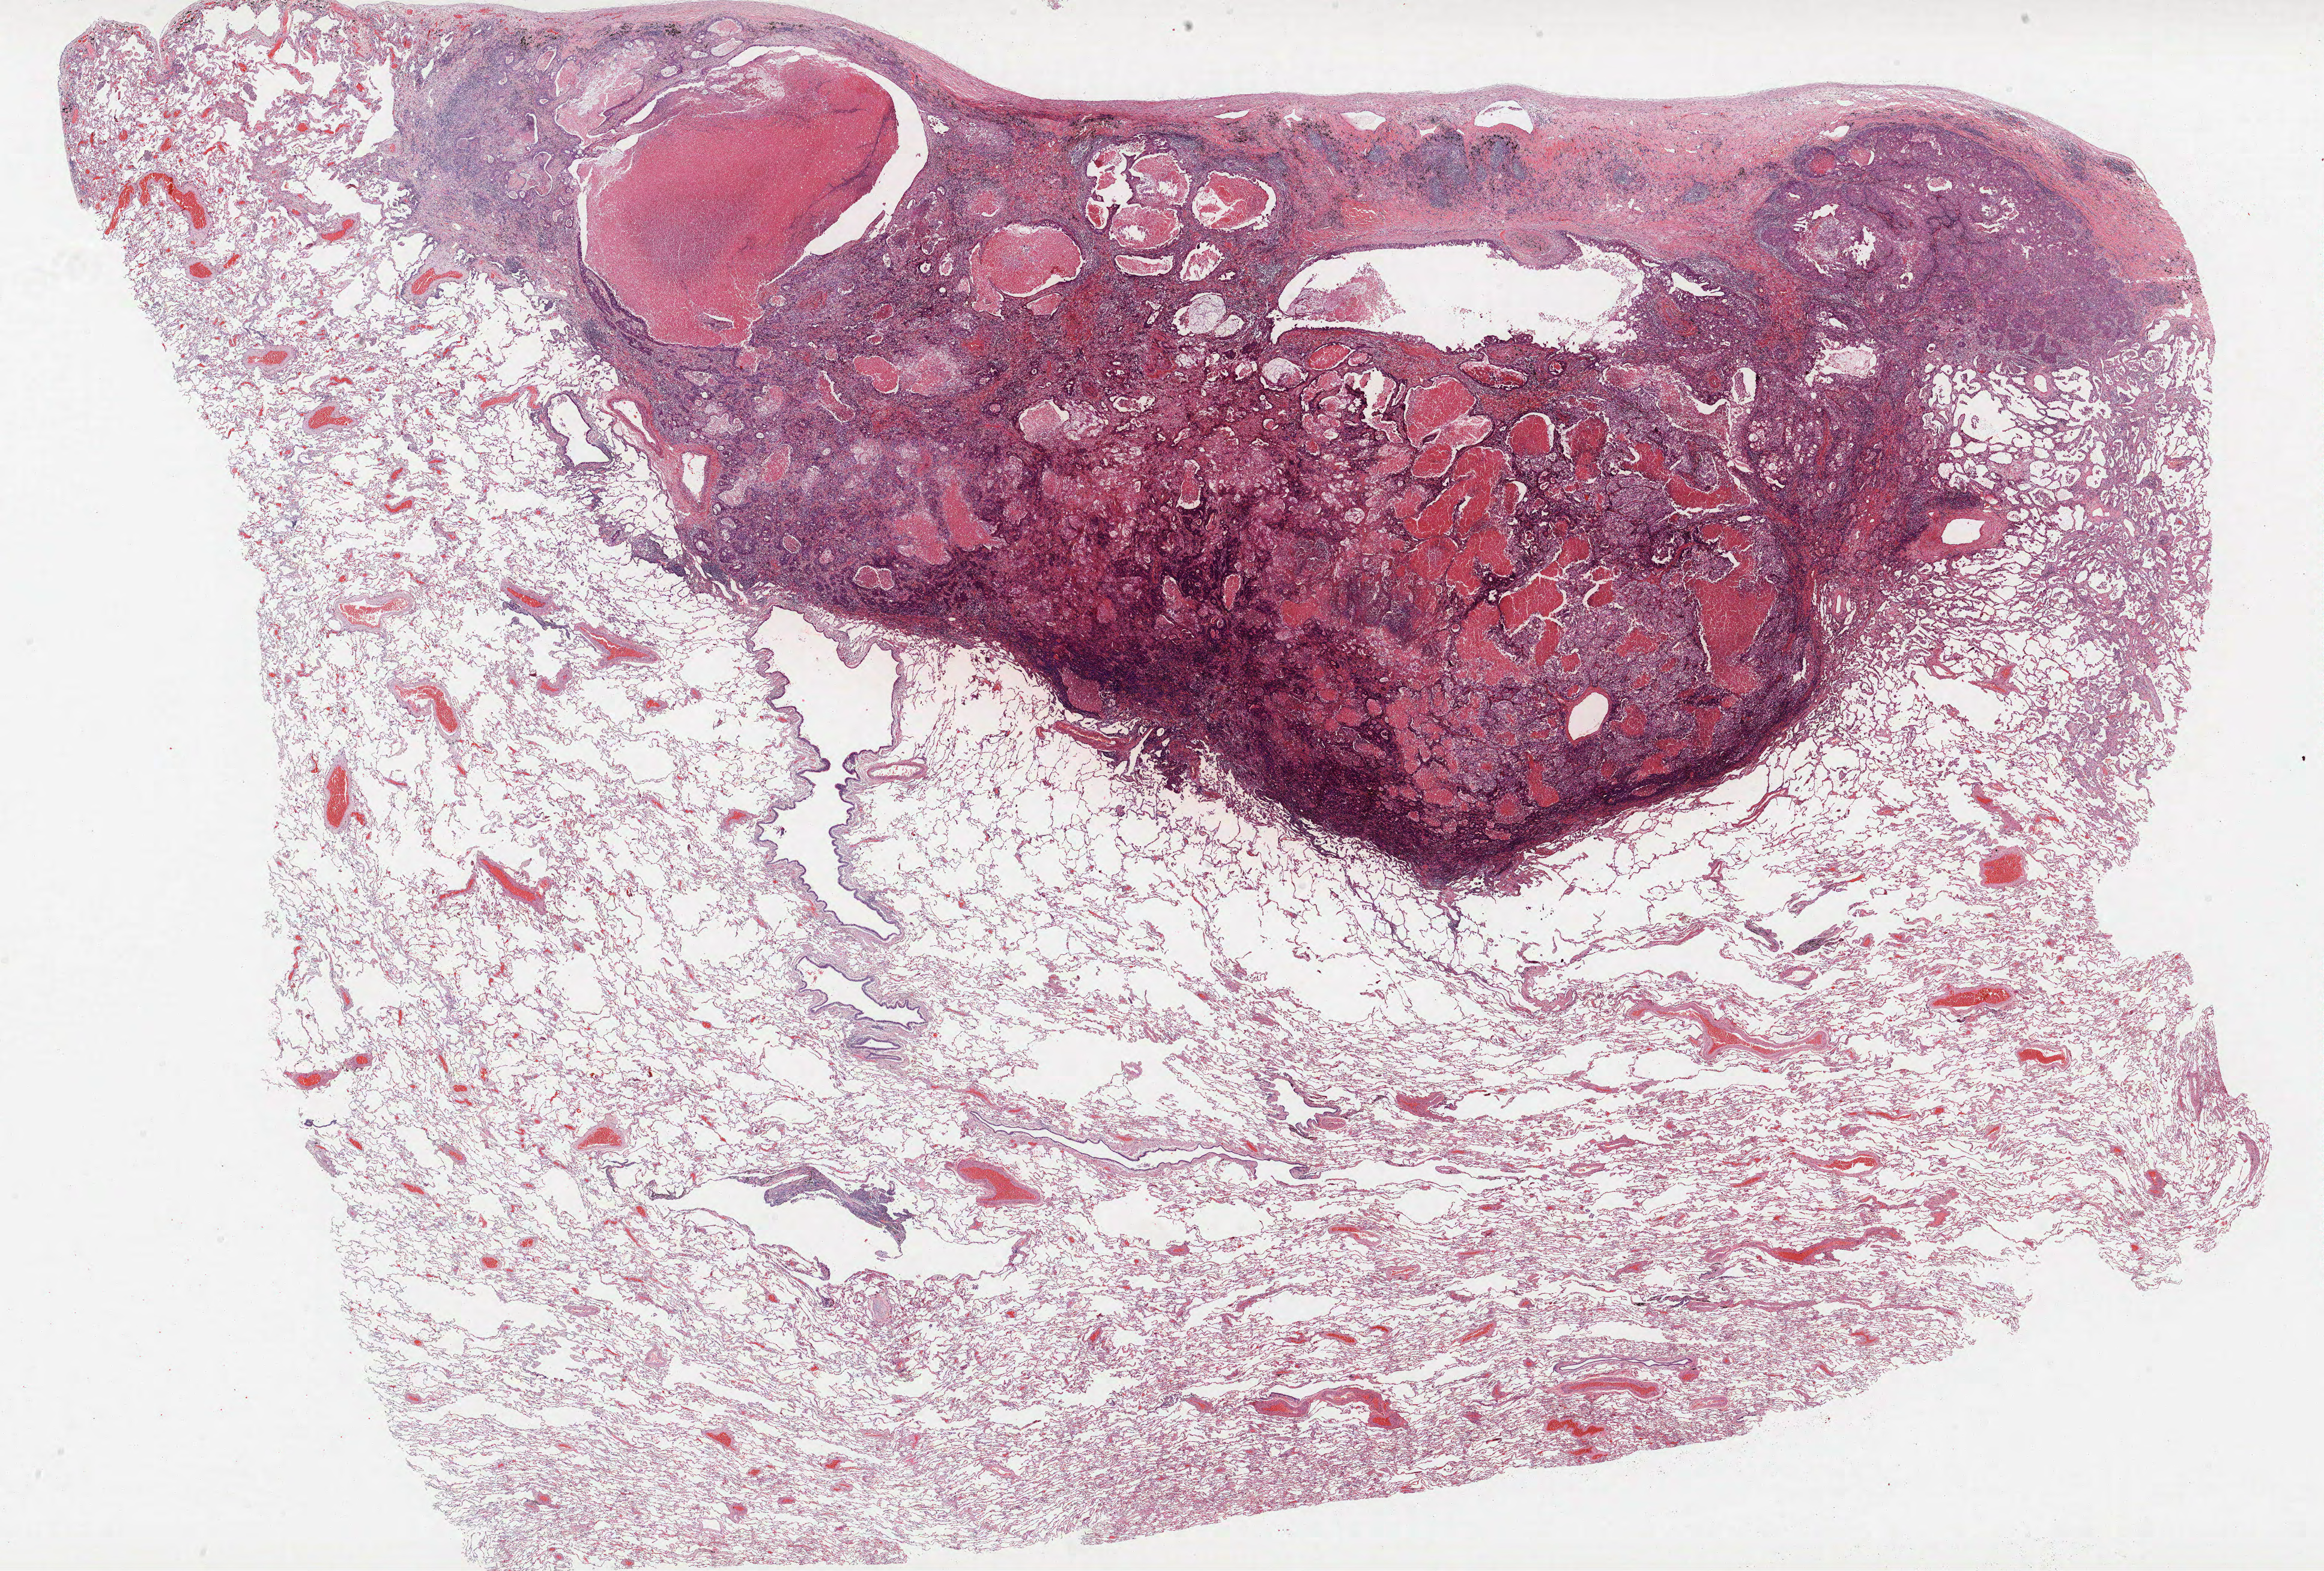
Whole-slide histology image, Hematoxylin and eosin (H&E) stained — low-resolution overview of the scanned area, about 31.0 x 20.9 mm (acquisition: 40x scan). FFPE section. Lung. Male patient, aged 61 at enrolment. Grade: poorly differentiated (G3).
Participant's lung-cancer diagnosis: Adenocarcinoma, NOS. Stage (AJCC 6th edition): IB. Primary tumour location (clinical record): left upper lobe. Tumour size (pathology): 35 mm.